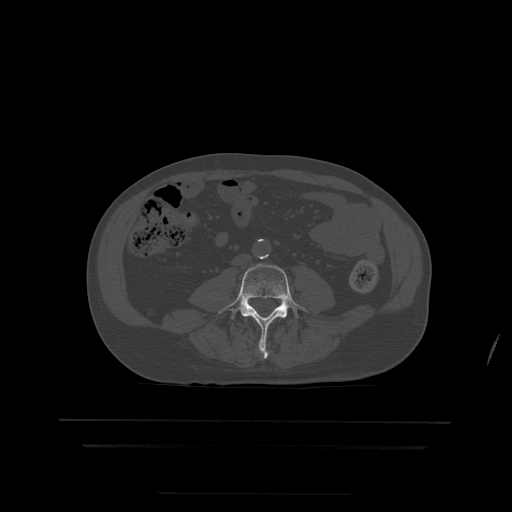
CT including the spine, one axial slice; slice 96 of 522 in the series (ordered by position); bone window (W 1800 / L 400 HU); 1.25 mm slice thickness; 512 × 512 image matrix. Patient age 68 years. From the clinical record (not read from this slice): primary cancer: urothelial.
Outlined on this slice (semi-automatic segmentation, software-assisted and operator-edited):
- L4 vertebra: bounding box <219,264,308,359> (left, top, right, bottom; pixels)